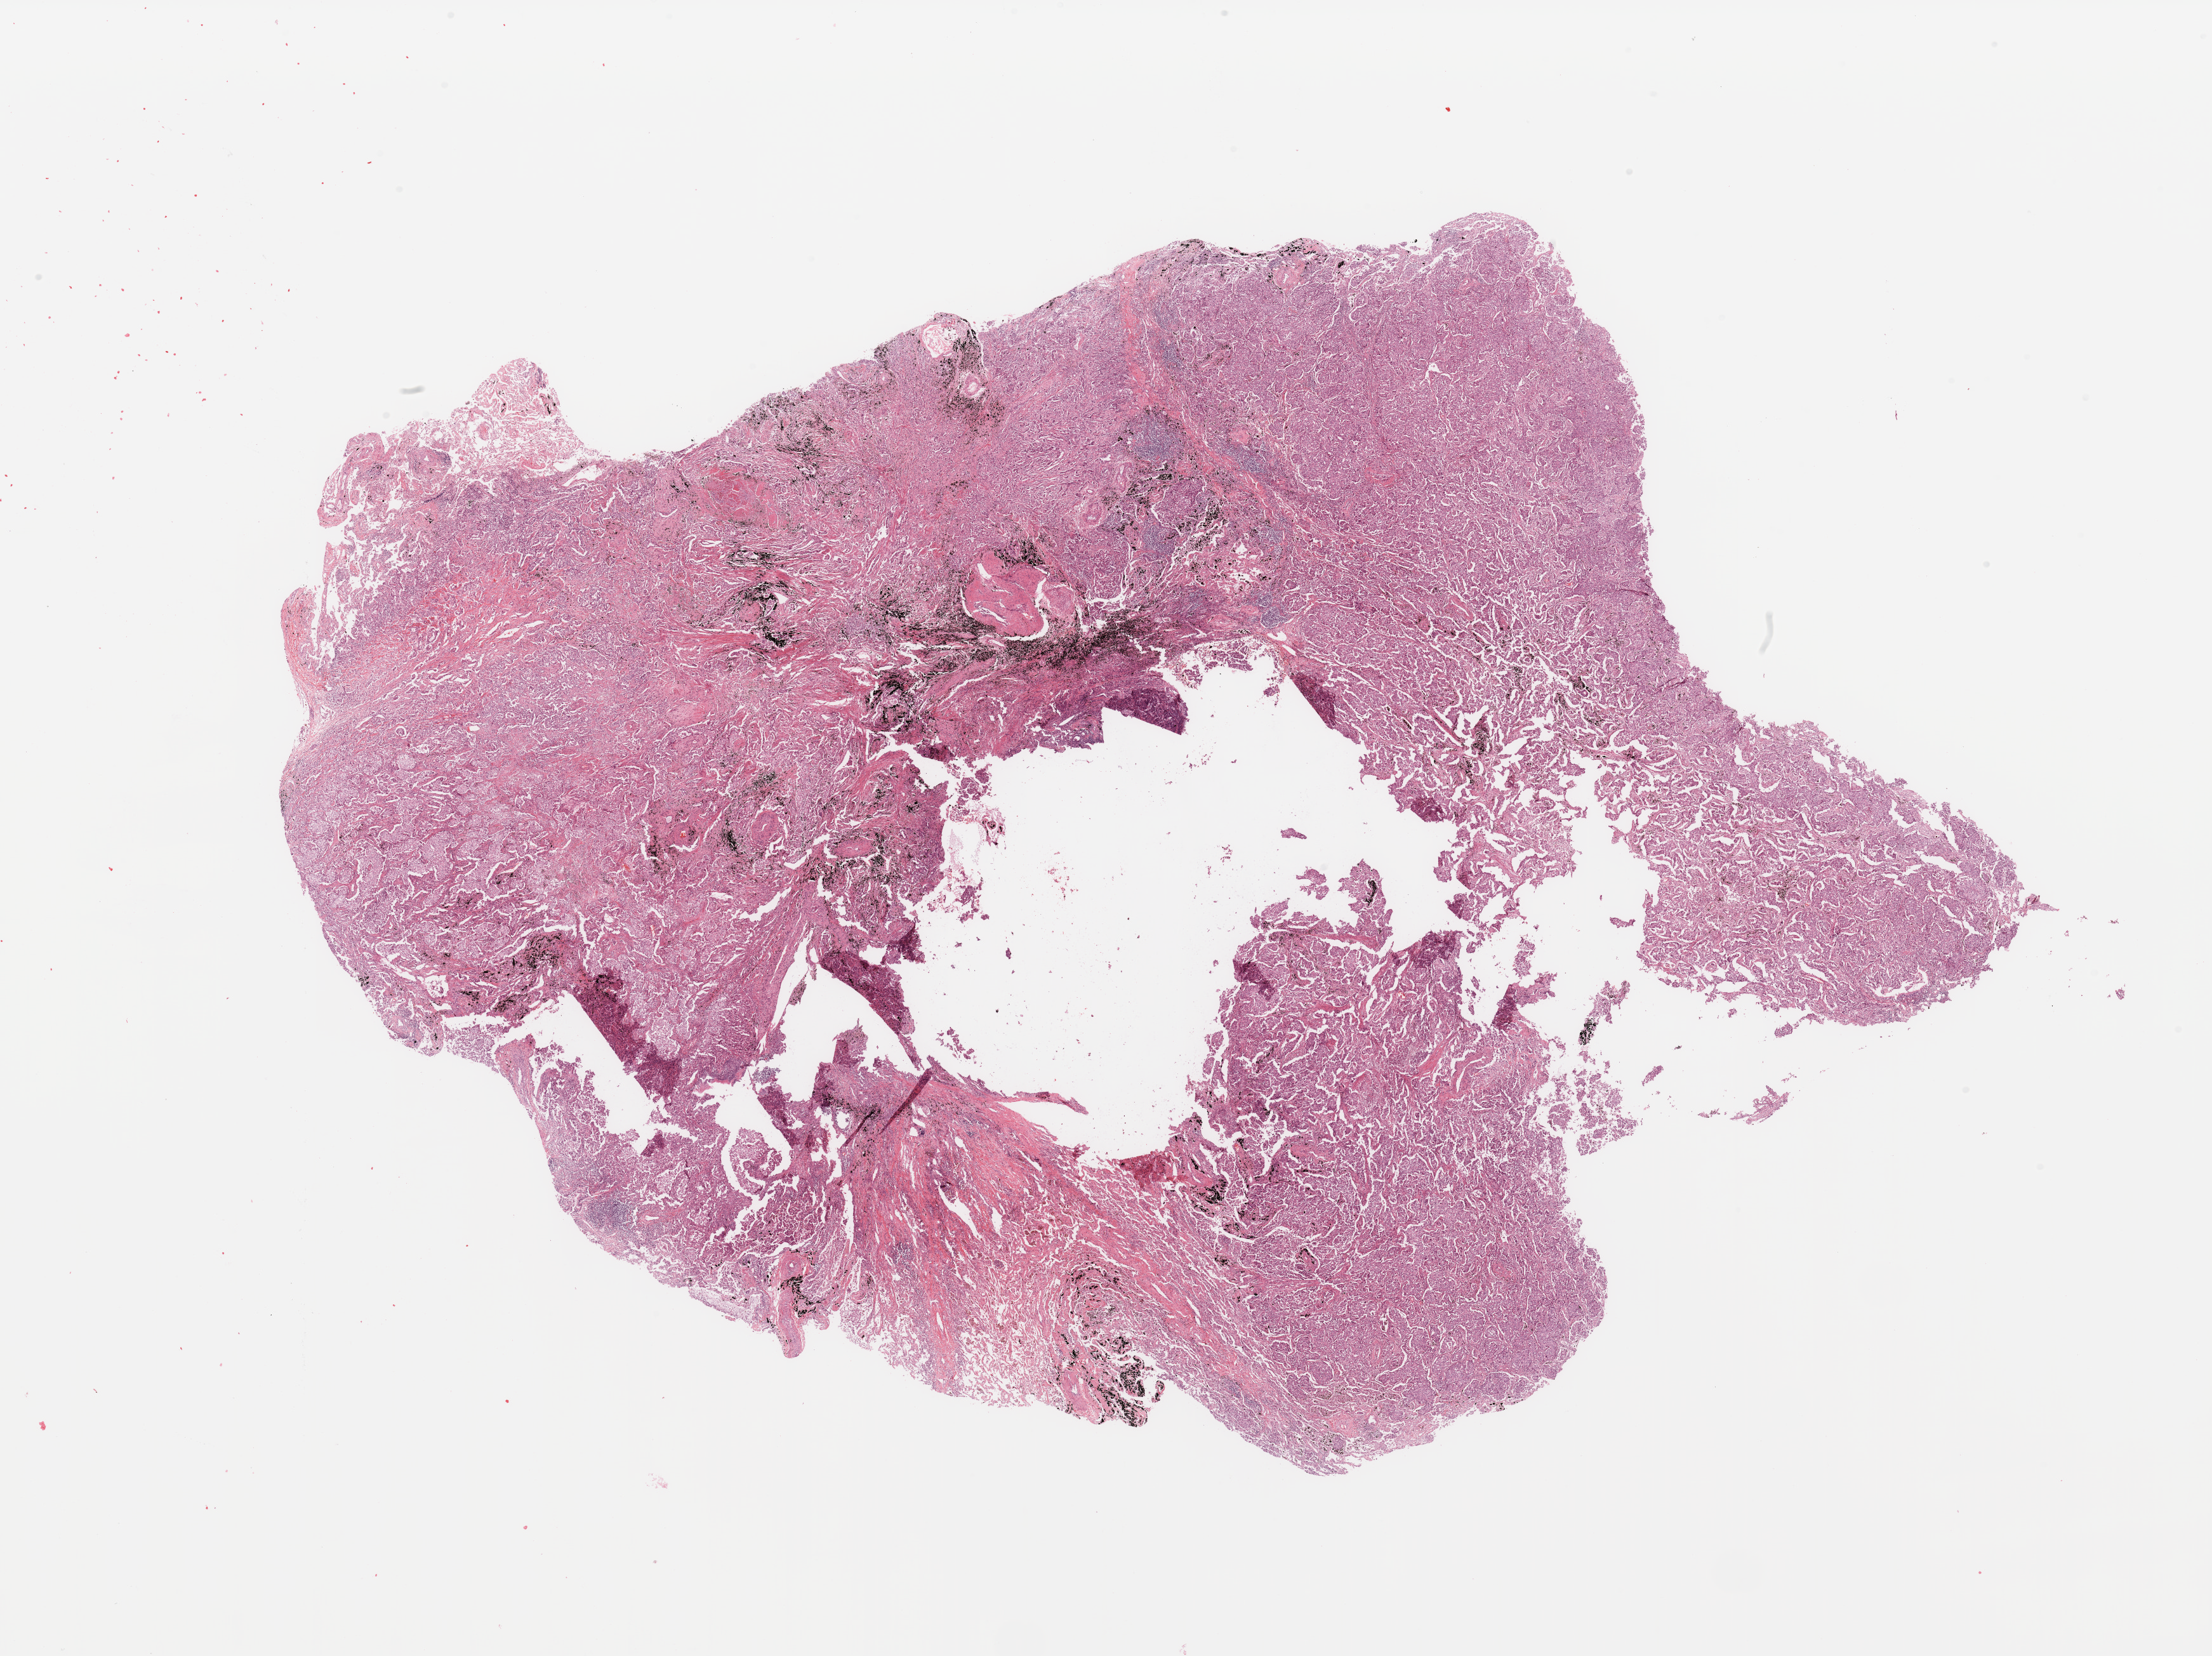
Whole-slide histology image, H&E-stained, whole scanned area (about 27.6 x 20.6 mm, slide scanned at 20x) shown as a low-resolution overview; tumour tissue sample, sampled site: lung. 54-year-old male patient. Histologic grade: G3 (poorly differentiated). Pathologist review of this section (percent, as recorded): tumour nuclei 70%, necrosis 3%.
- diagnosis: Adenocarcinoma, NOS
- AJCC pathologic stage: IB